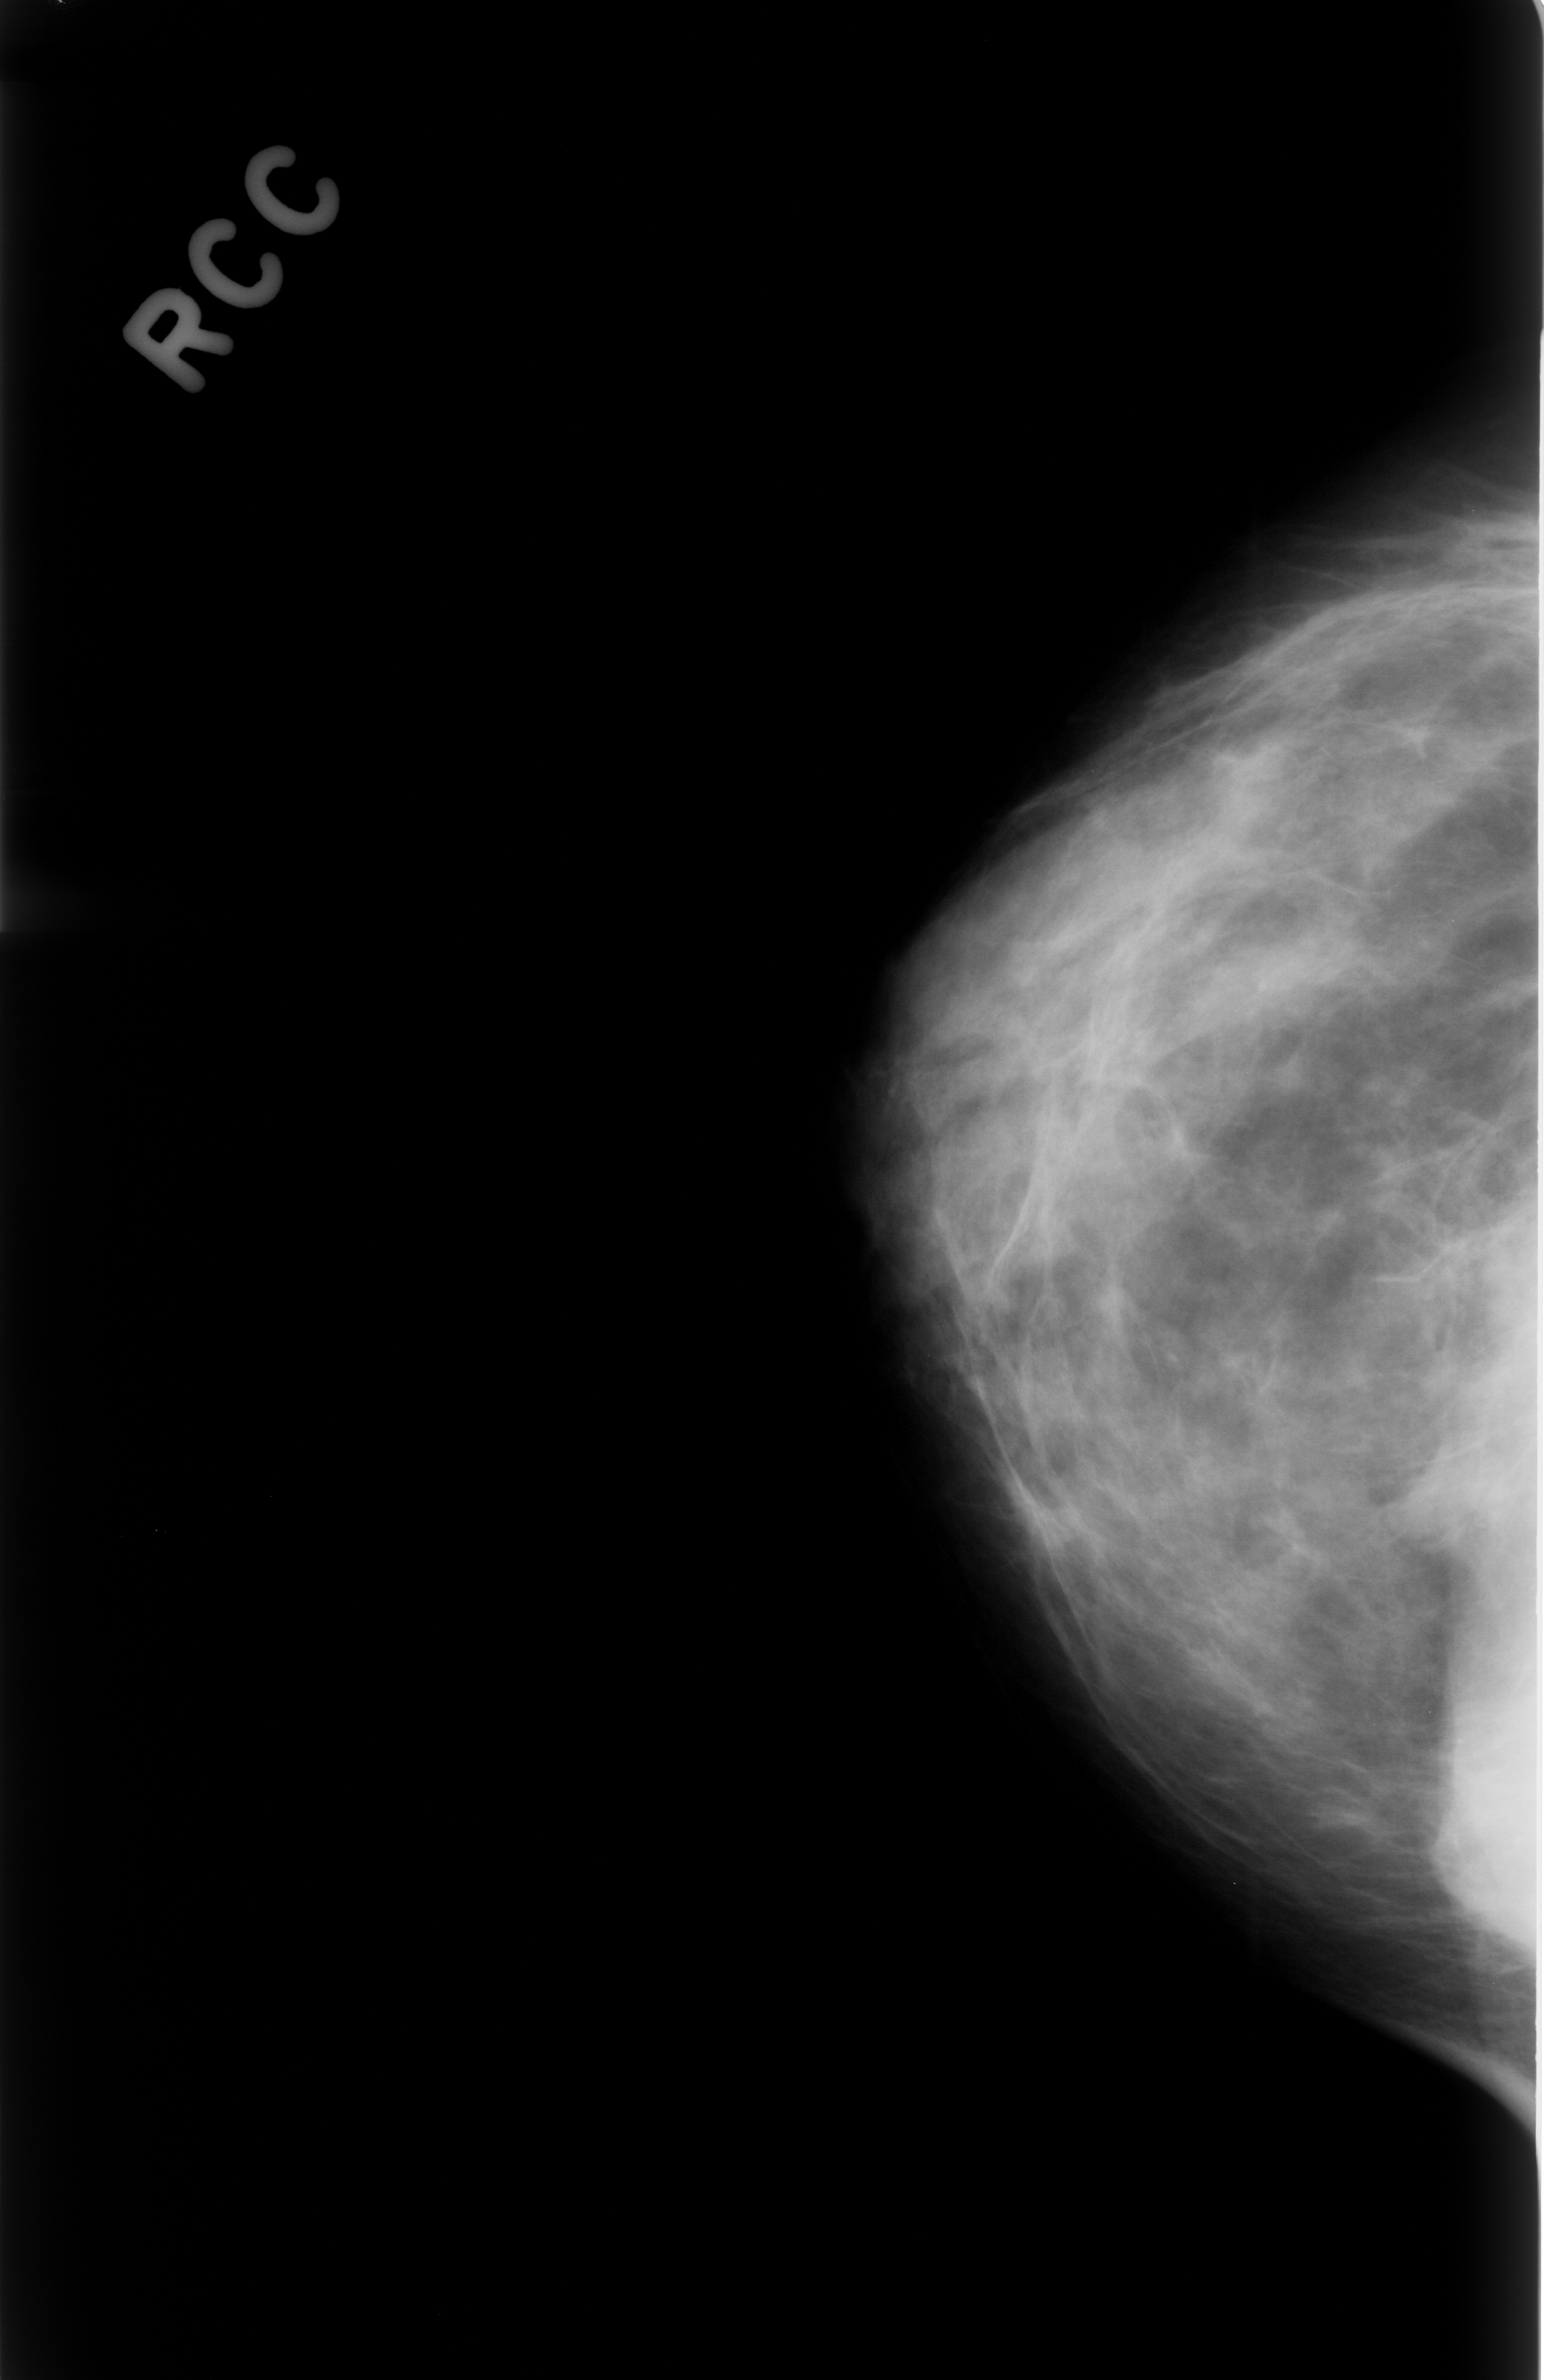
Mammogram (digitized film). Right breast. CC view. Breast composition: heterogeneously dense (BI-RADS density category 3 of 4). 1544 × 2380 image matrix.
Expert-marked regions of interest on this image (one box per marked abnormality):
- mass, shape oval, margins ill defined; BI-RADS assessment category 4; pathology result (as recorded, not read from the image): benign: box from (x=1375, y=1436) to (x=1508, y=1564) px